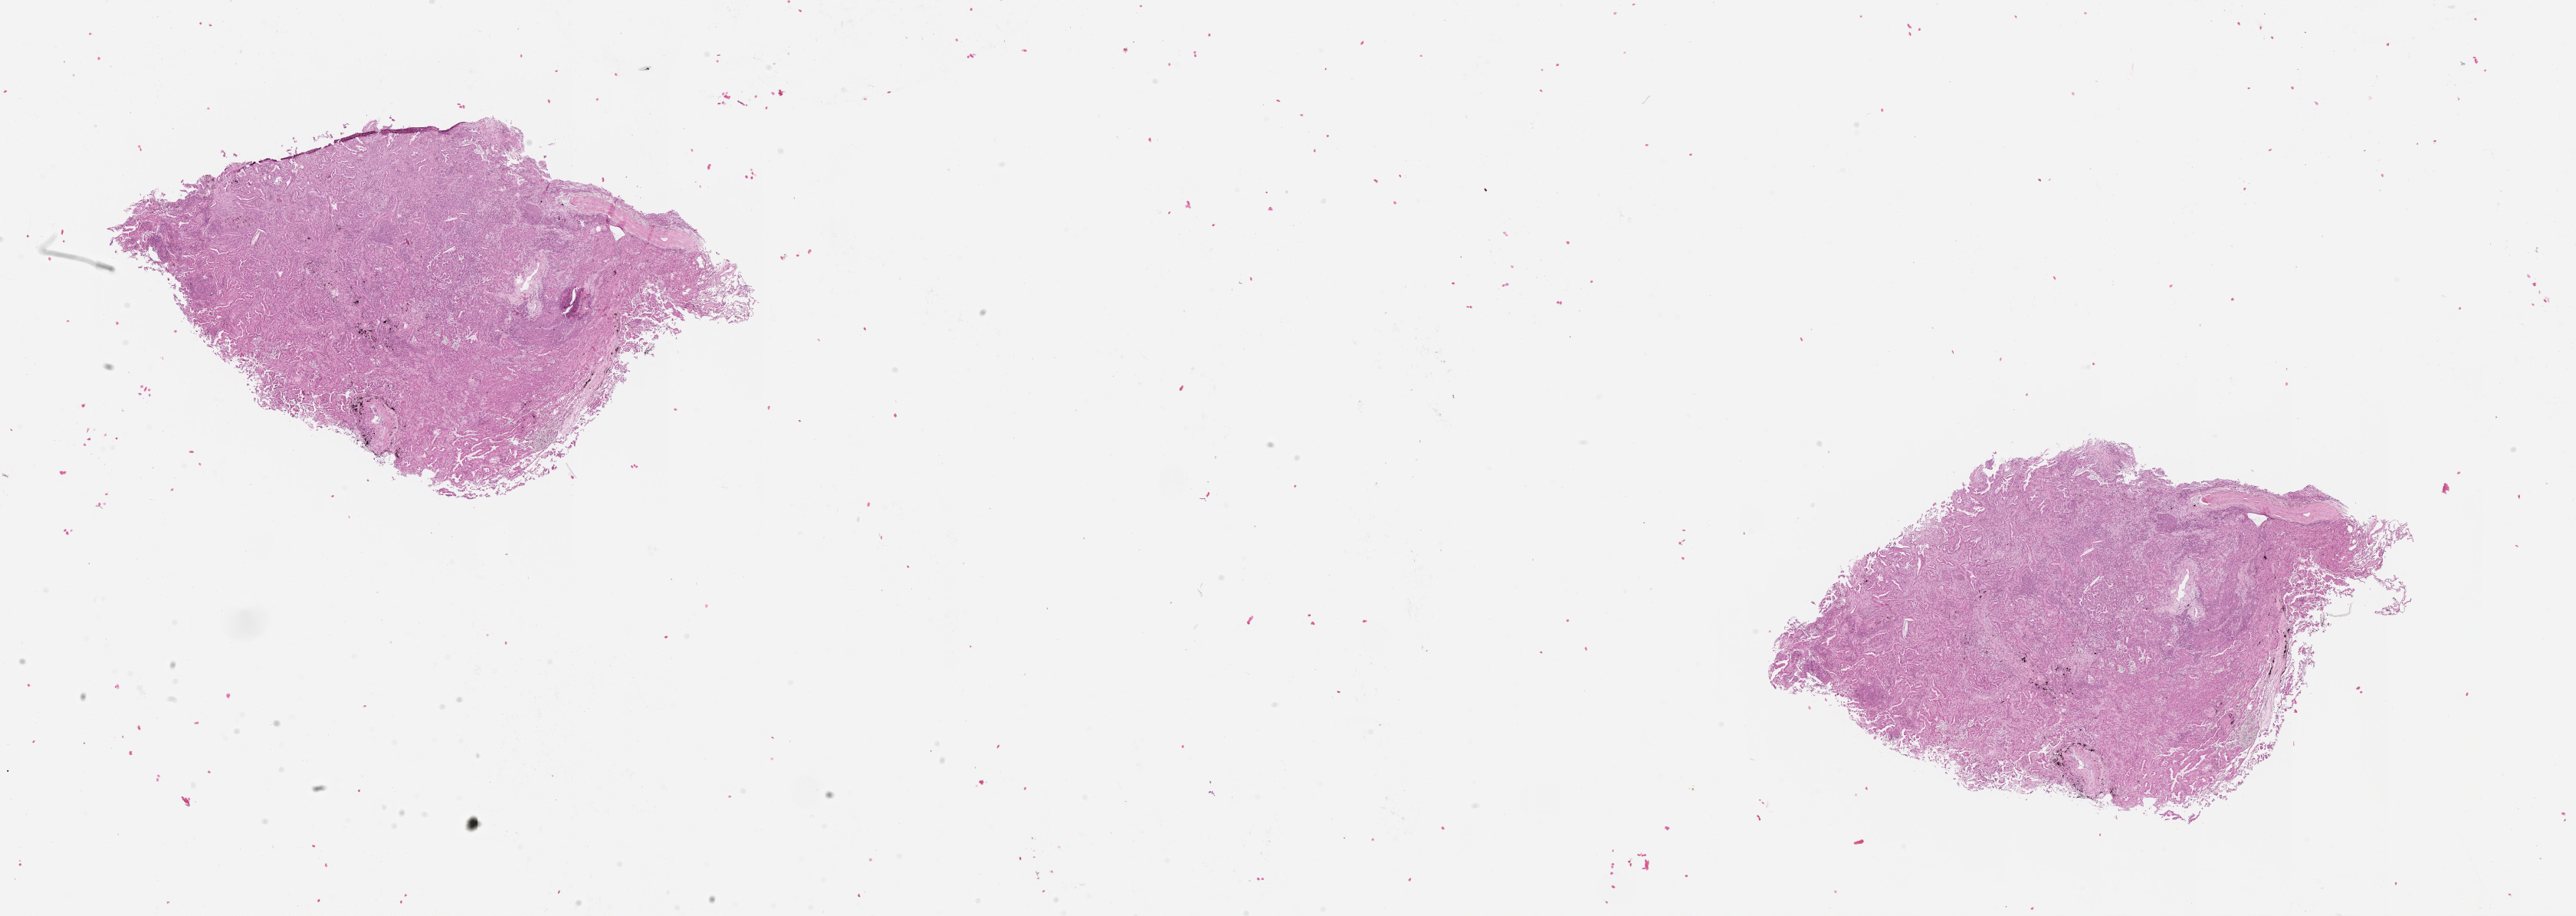
Digitized H&E-stained tissue section (whole slide), whole scanned area (about 27.1 x 9.6 mm, acquisition: 20x scan) shown as a low-resolution overview. Lung, tissue type not recorded.
Patient diagnosis (cohort enrolment): lung adenocarcinoma (lung).